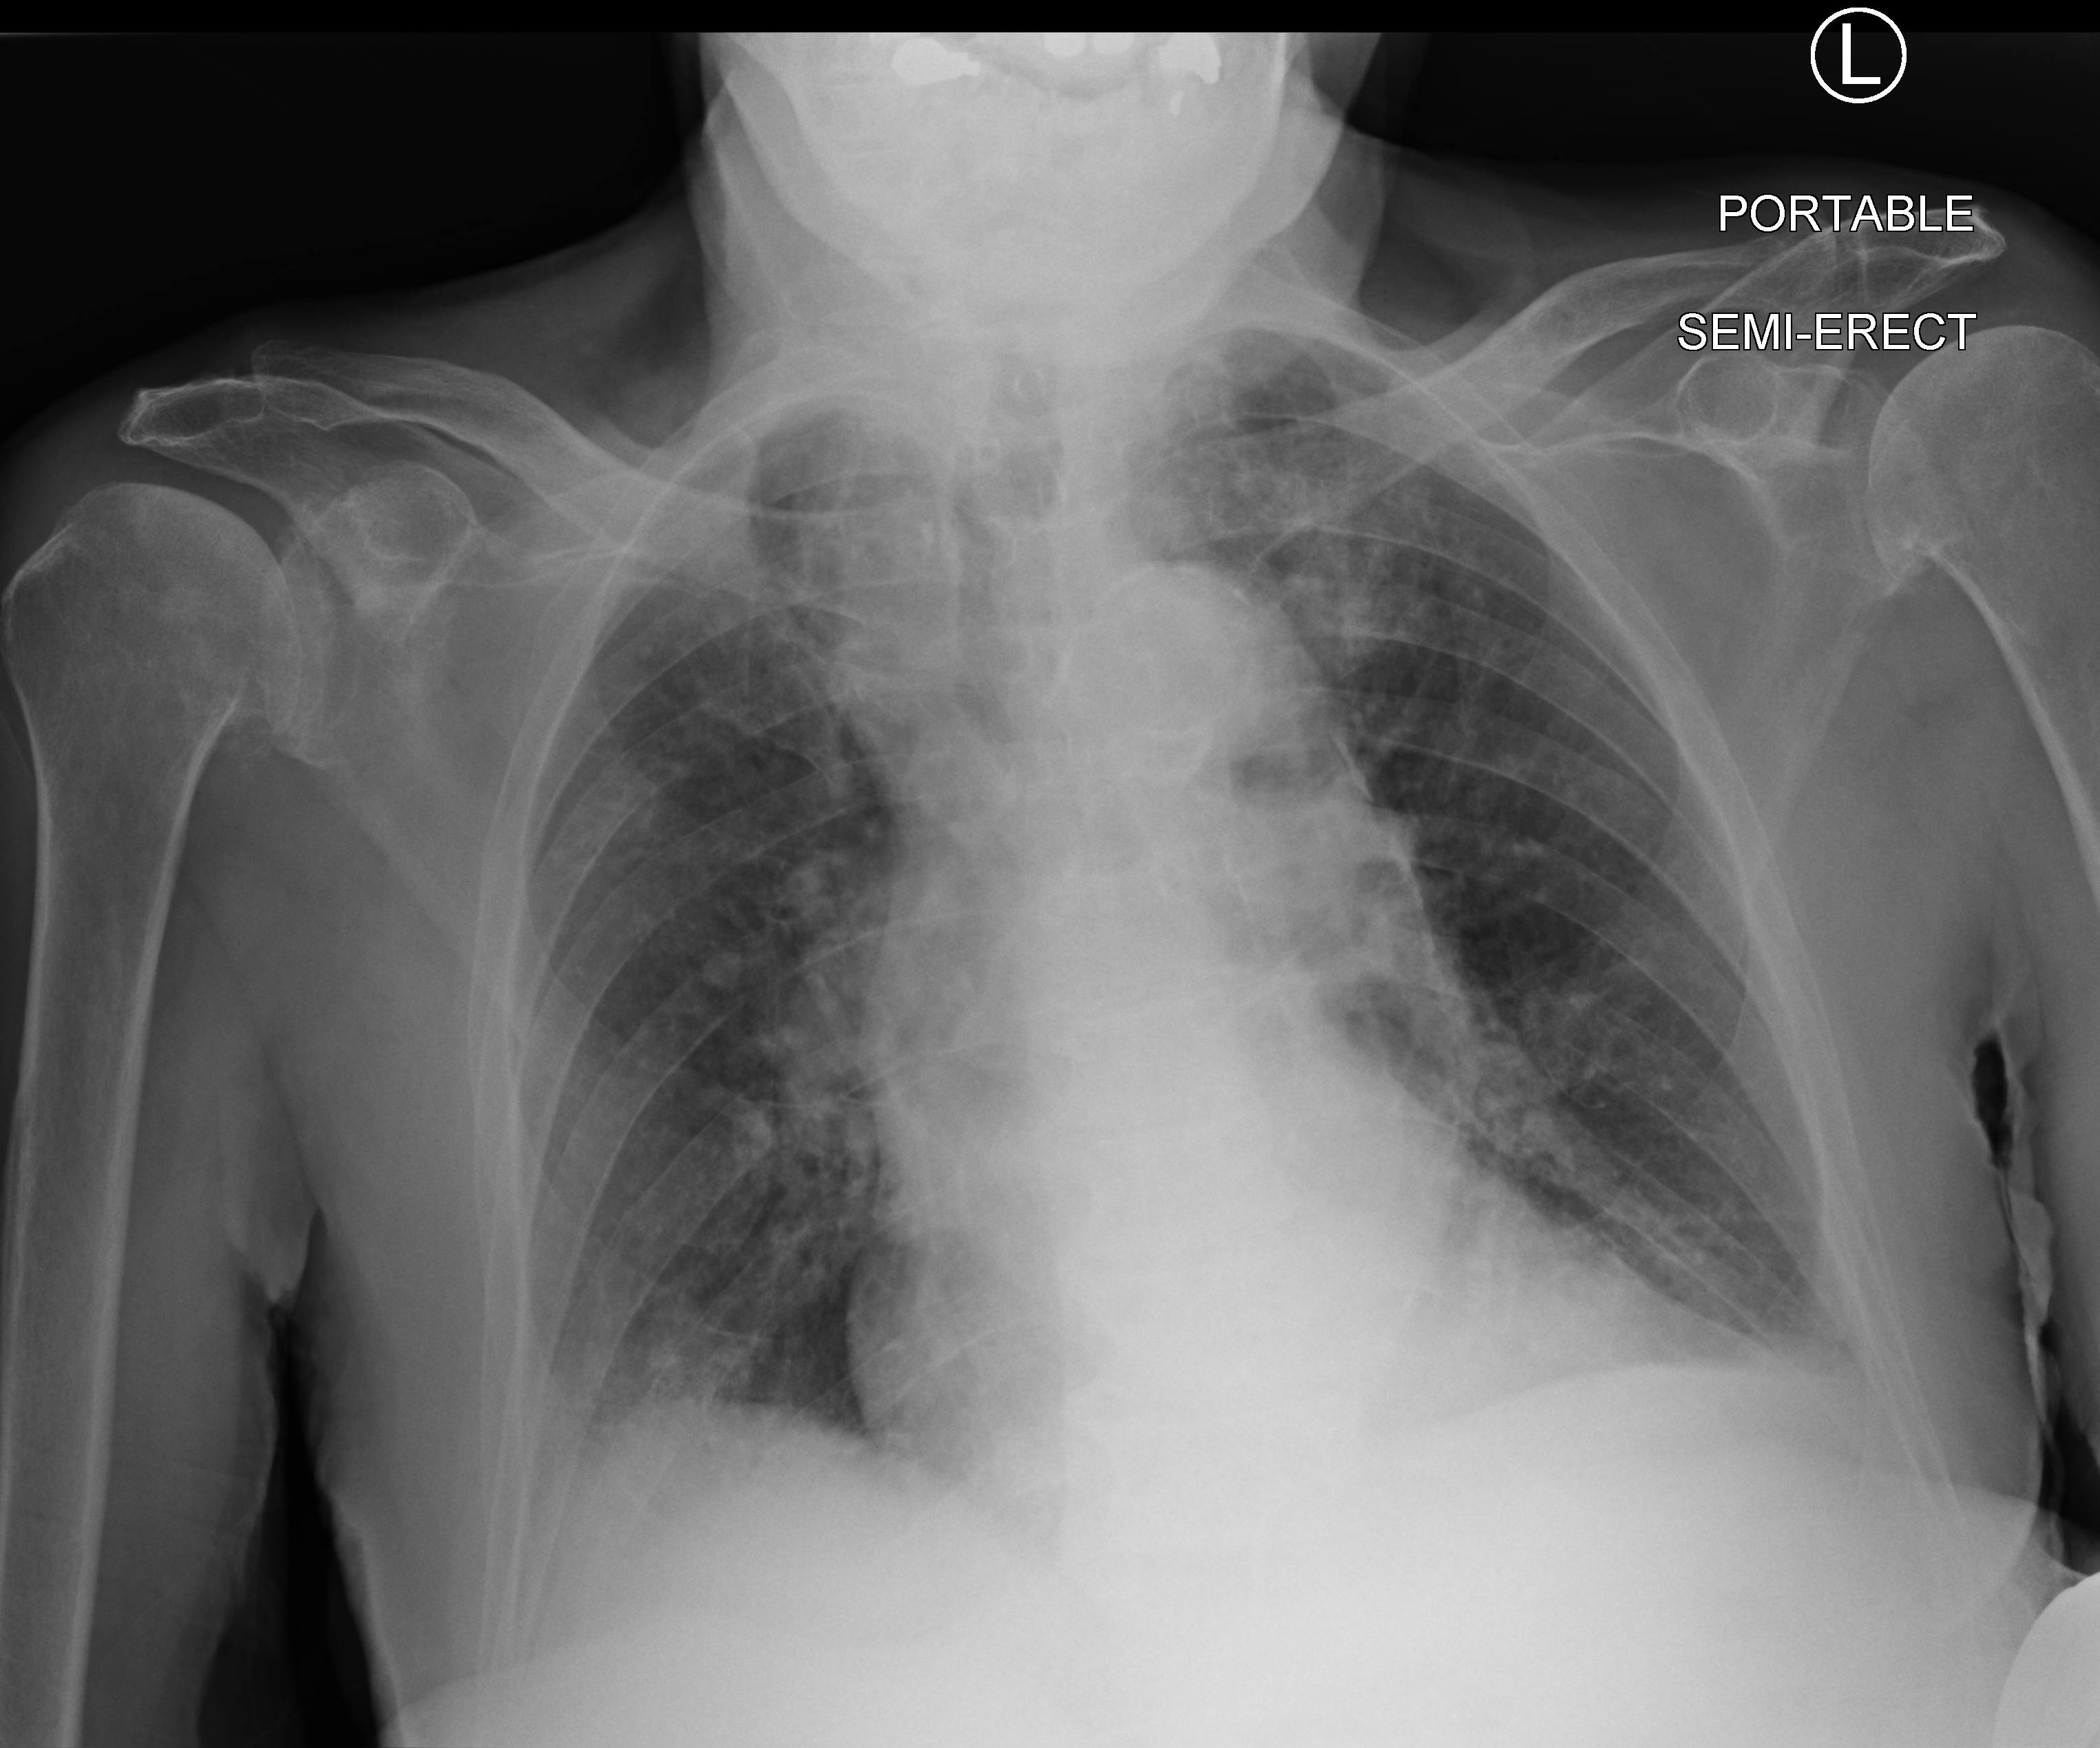
Portable chest radiograph. Male patient hospitalised with COVID-19, age 75–90 years.
Admission-level facts for this patient (not findings on this image; timing relative to this image not recorded): admitted to intensive care during this hospital stay: no; length of hospital stay: 7 days; mechanically ventilated during this hospital stay: no.